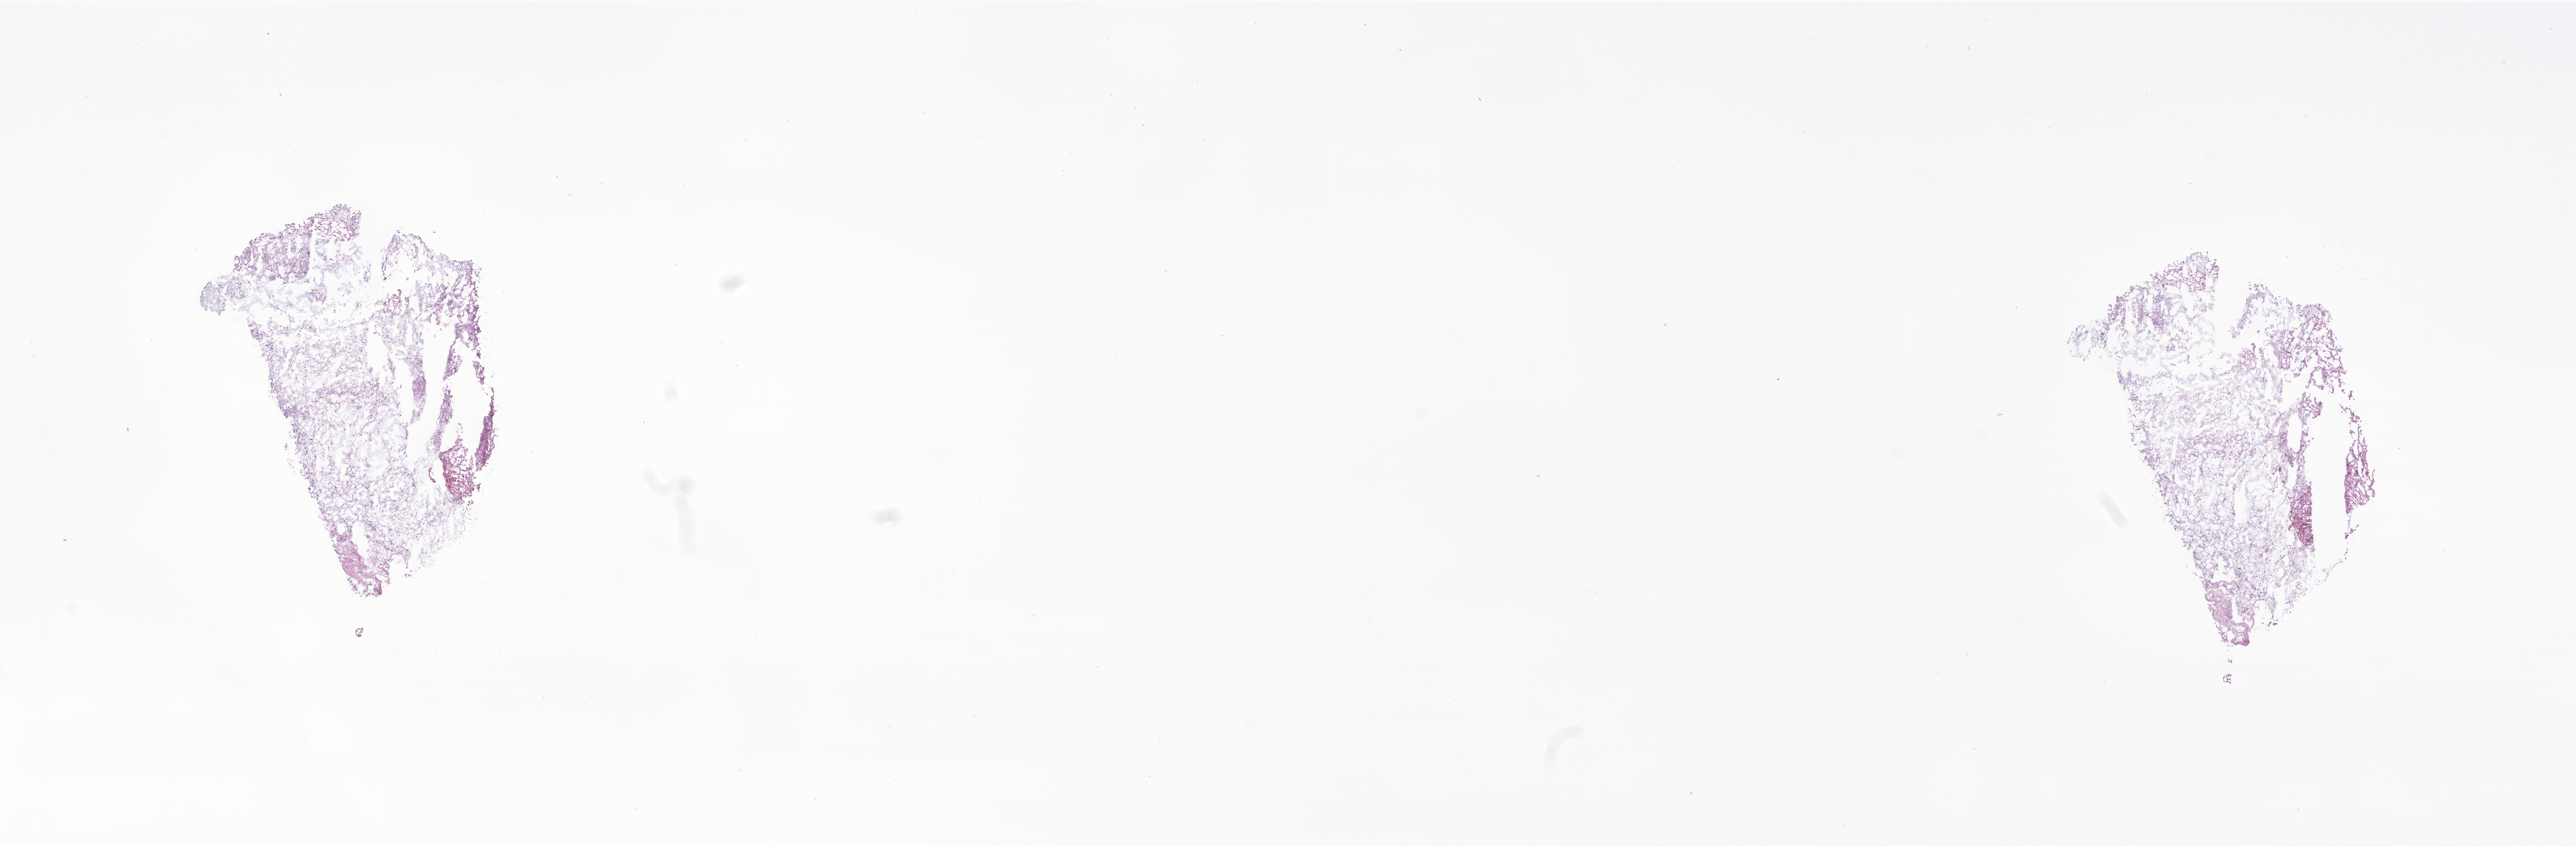
Hematoxylin and eosin (H&E) whole-slide image of tumor tissue from the optic nerve — shown as a low-resolution overview of the whole scanned area (about 23.5 x 7.7 mm). Cryosection (OCT / tissue freezing medium). Patient: male, age 143 months (11 years 11 months).
Diagnosis: Glioma, malignant.